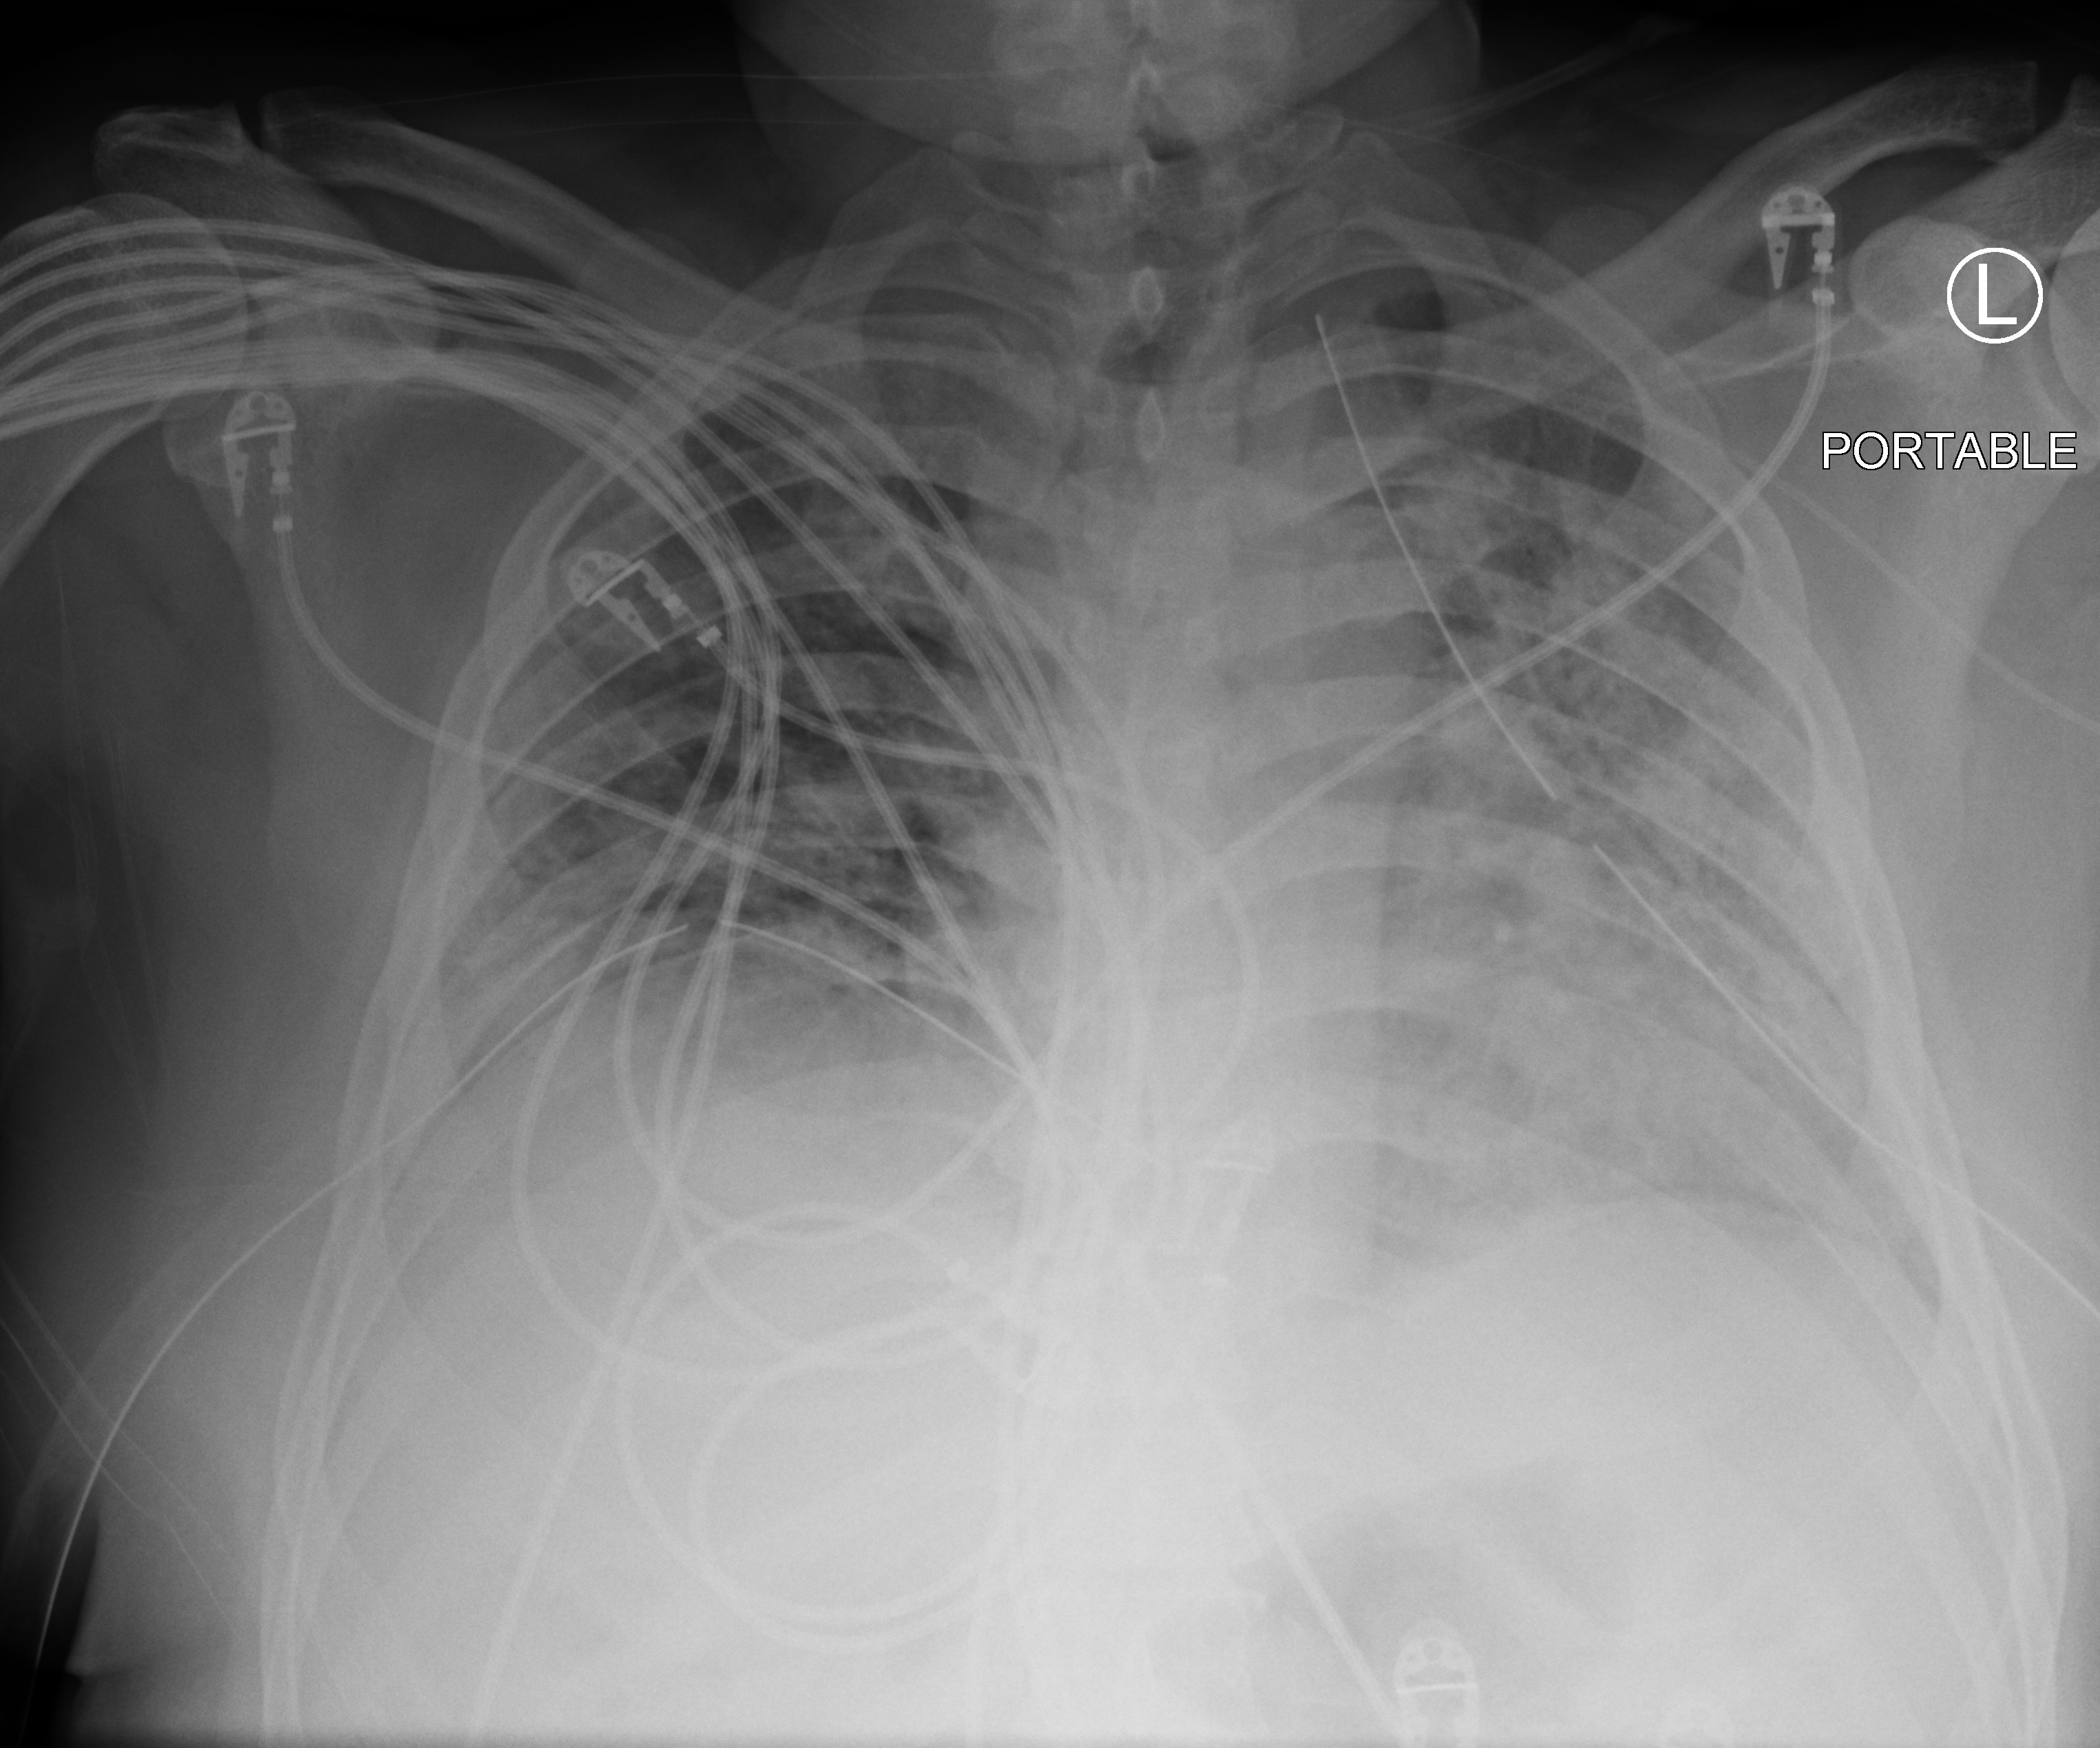
Portable chest radiograph, anteroposterior (AP) projection. Patient hospitalised with COVID-19; male, aged 18–59 years.
Admission-level facts for this patient (not findings on this image; timing relative to this image not recorded): length of hospital stay: 29 days; mechanically ventilated during this hospital stay: yes; admitted to intensive care during this hospital stay: yes.